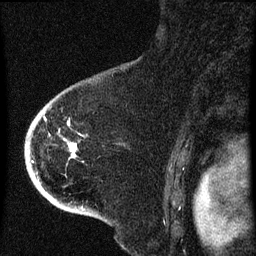
Breast MRI (dynamic contrast-enhanced), one sagittal slice. Position 49 of 60 along the scan axis. Dynamic contrast-enhanced series, image 2 of 4 at this slice position (ordered by acquisition). 1.5 T. TE 4.2 ms, TR 8 ms. 256 × 256 image matrix, field of view 180 × 180 mm. Patient: female, 71 years.
Annotated regions visible in this slice (semi-automatically segmented with operator editing):
- analysis volume of interest (the breast-tissue region the enhancement analysis was run in; not a lesion): bounding box [x1, y1, x2, y2] px = [32, 86, 125, 205]
- tumour enhancement mask (voxels above the 70 % enhancement threshold inside the analysis volume of interest): [44, 118, 80, 153]